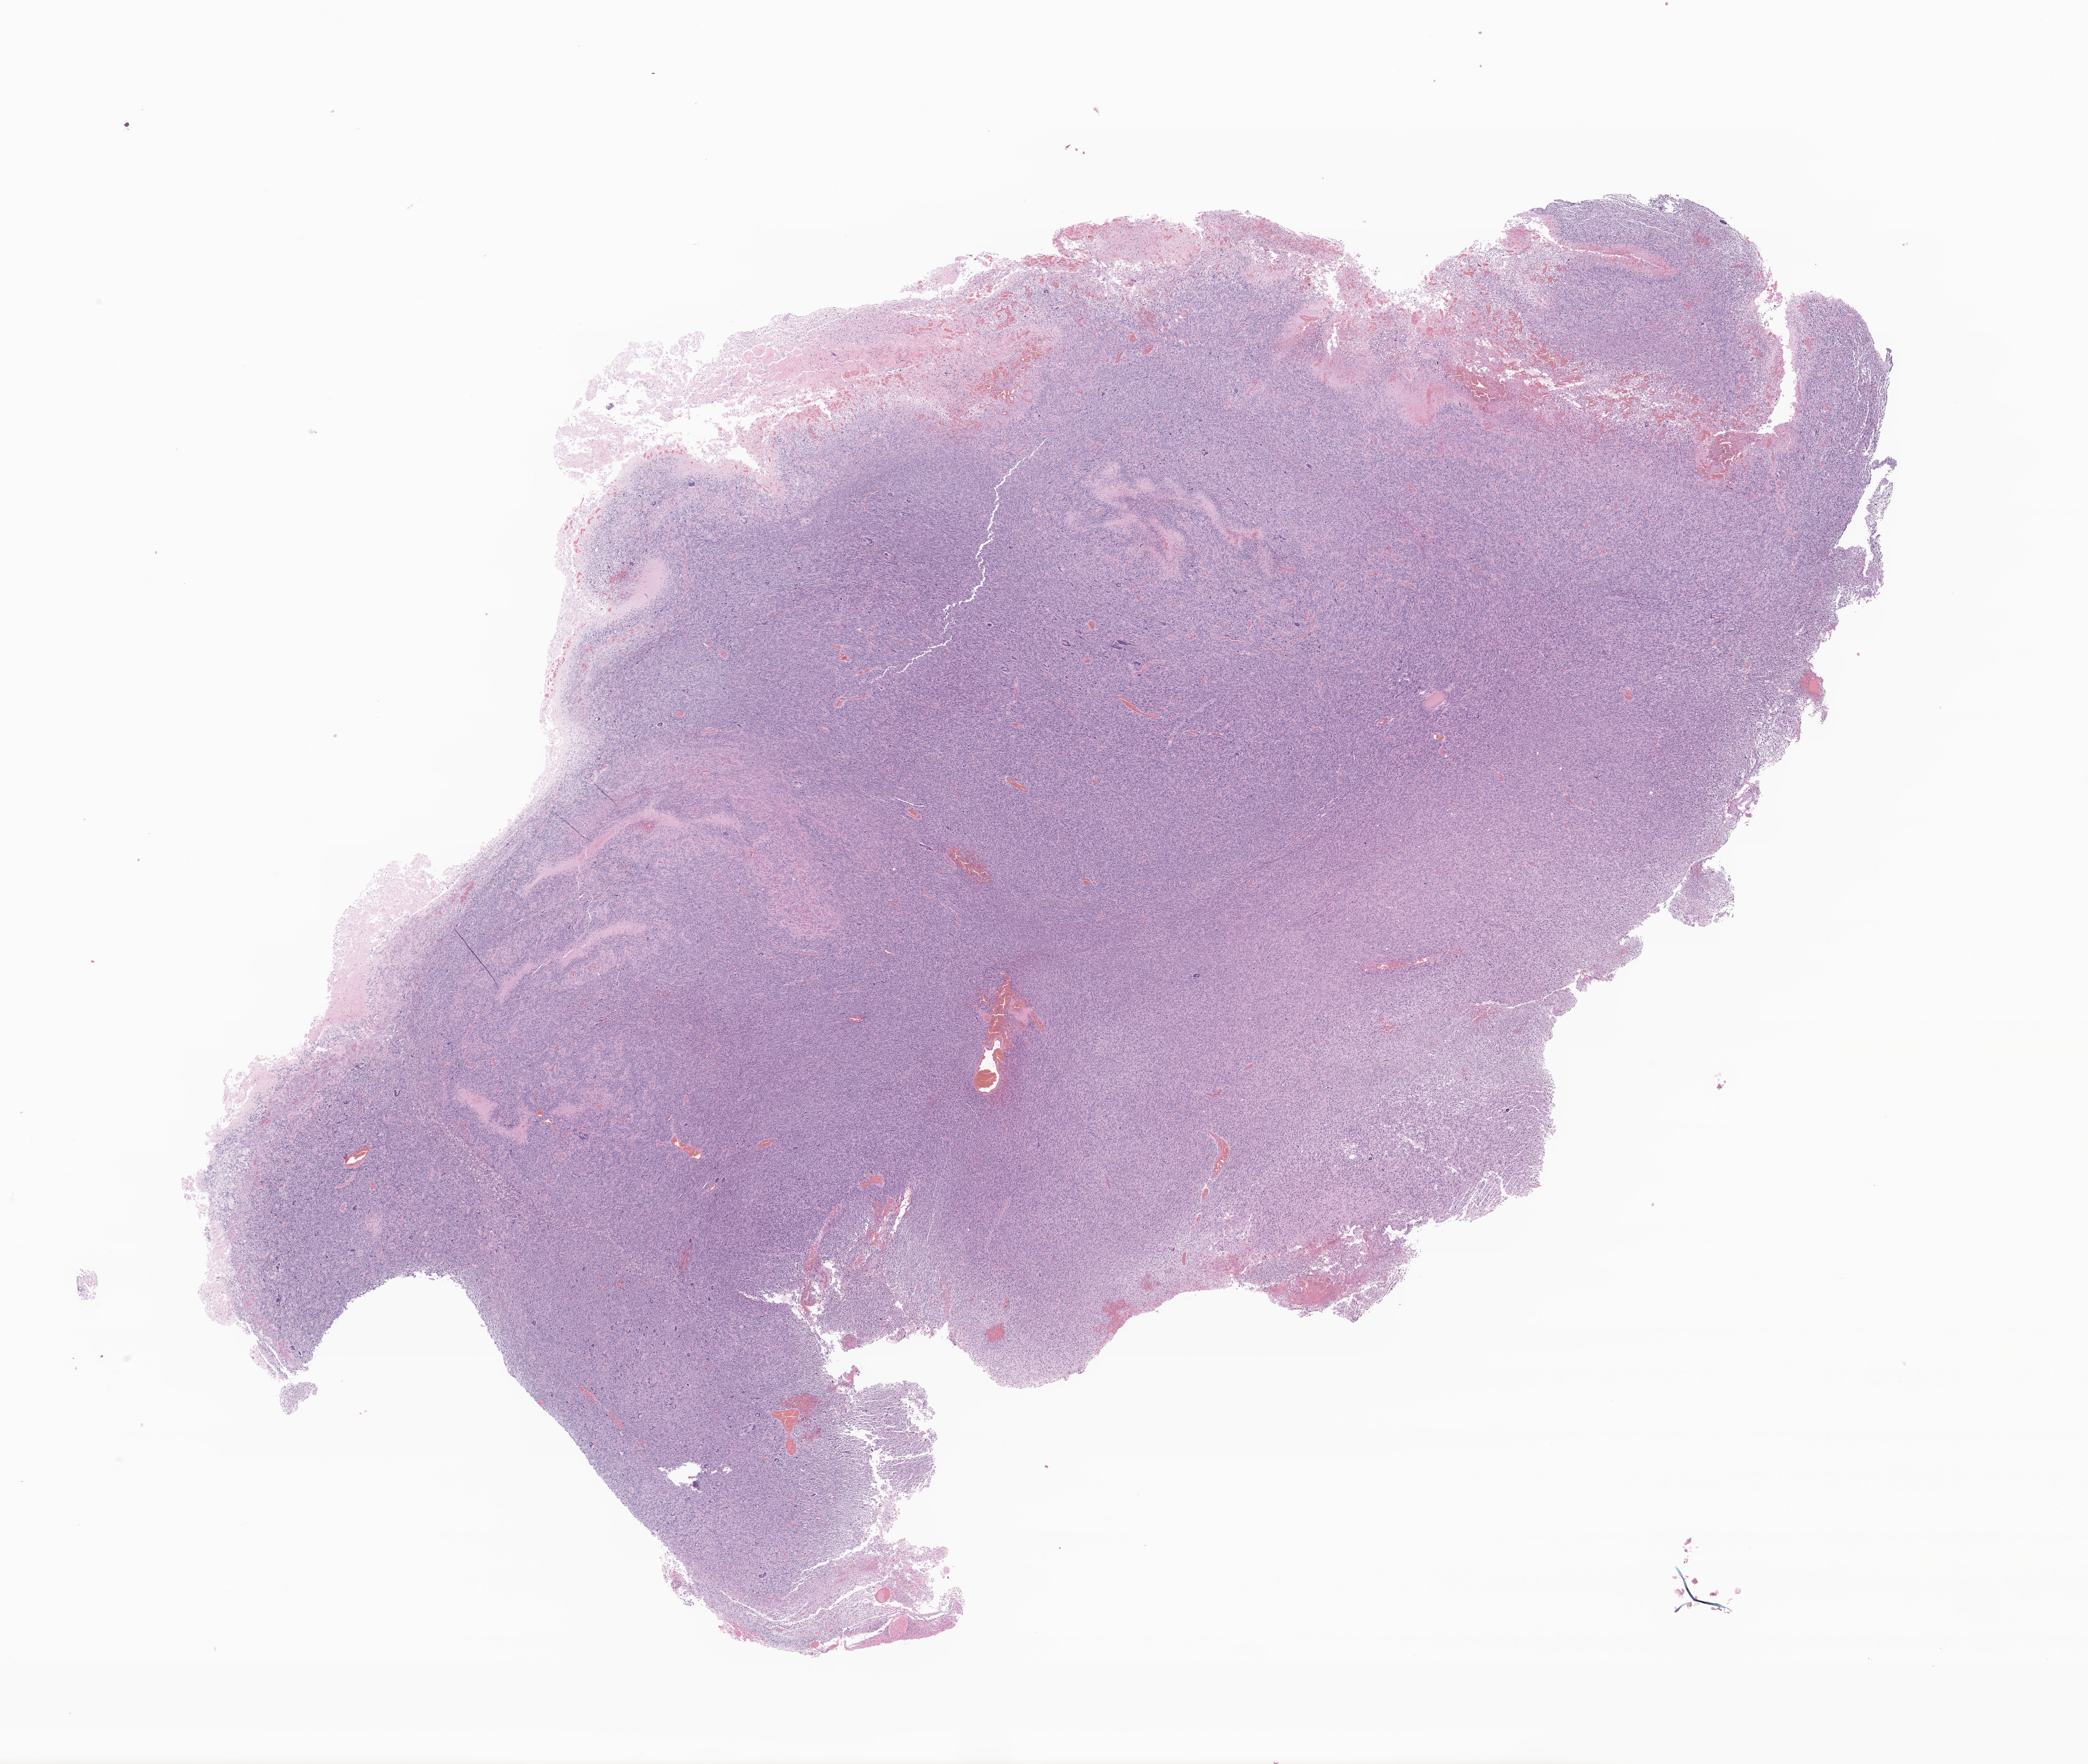
Whole-slide image, hematoxylin and eosin (H&E) stain of tumor tissue from the brain — whole scanned area (about 21.8 x 18.4 mm) shown as a low-resolution overview. Formalin-fixed, paraffin-embedded (FFPE) tissue. Patient female; age 276 months (23 years).
- recorded diagnosis: Glioma, malignant